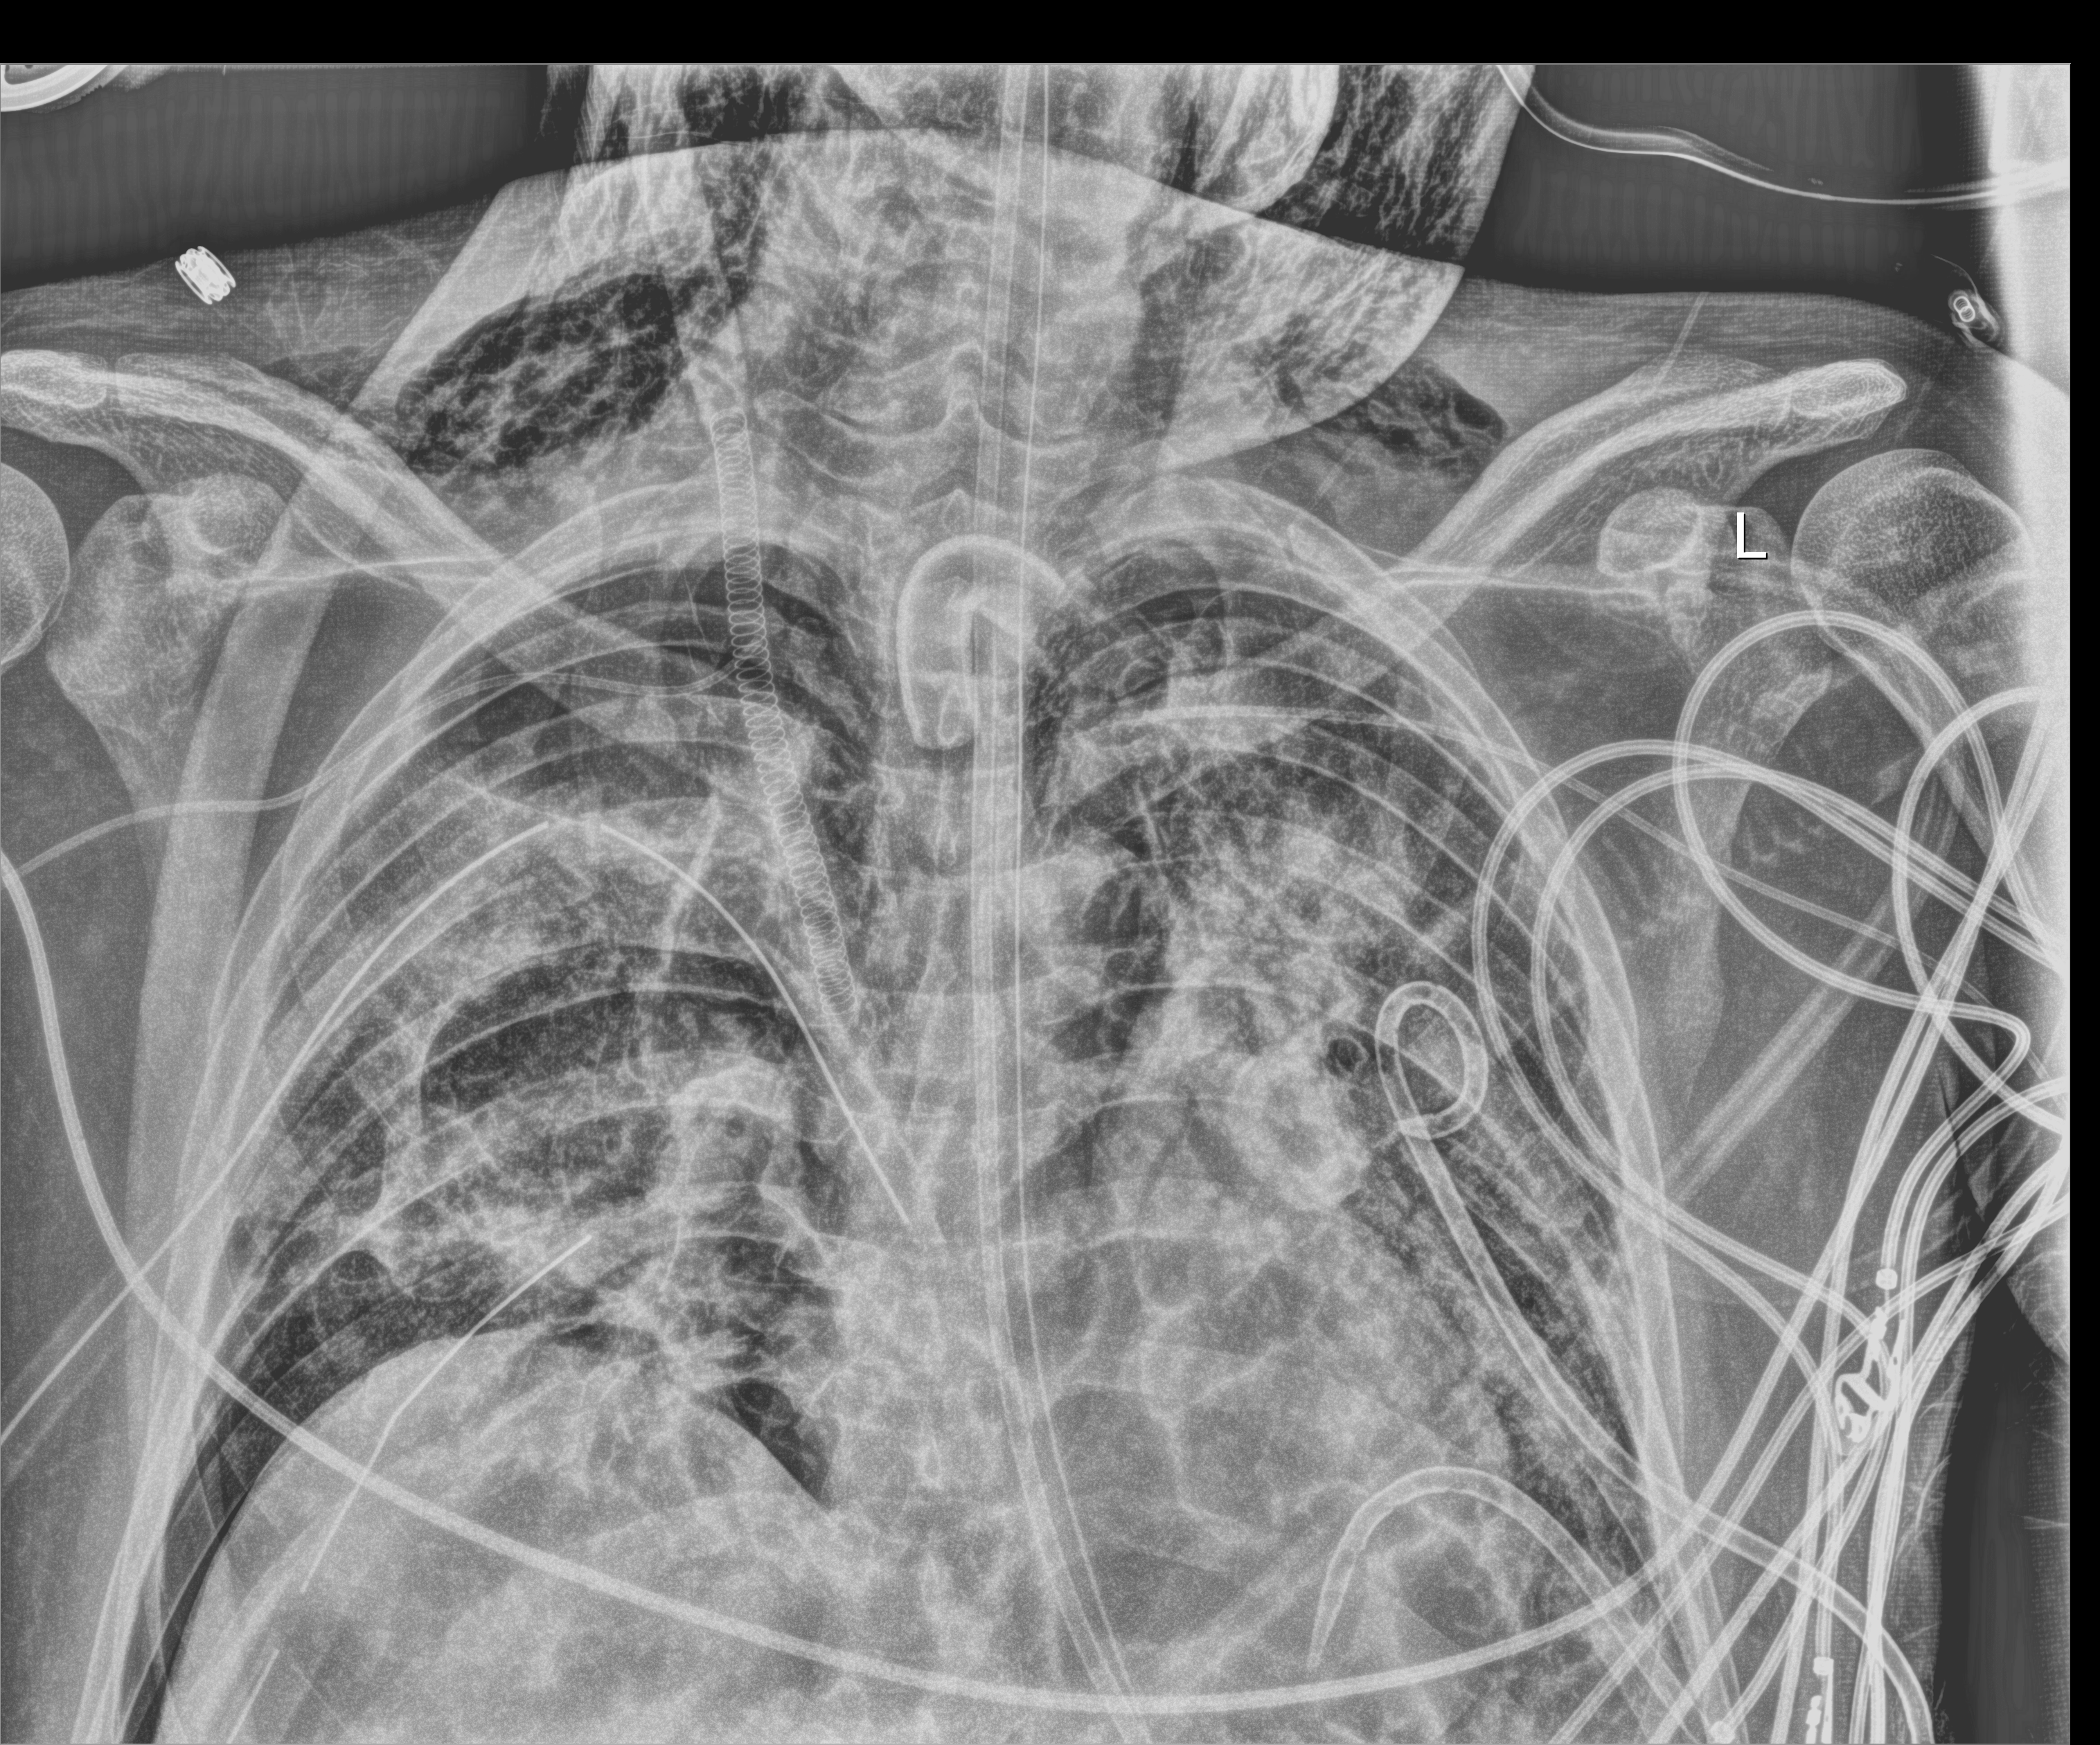
Chest radiograph (digital radiography); anteroposterior (AP) projection. Adult patient hospitalised with COVID-19, age 18–59 years.
Admission-level facts for this patient (not findings on this image; timing relative to this image not recorded): mechanically ventilated during this hospital stay: yes; admitted to intensive care during this hospital stay: yes; other chronic lung disease (admission record): no.